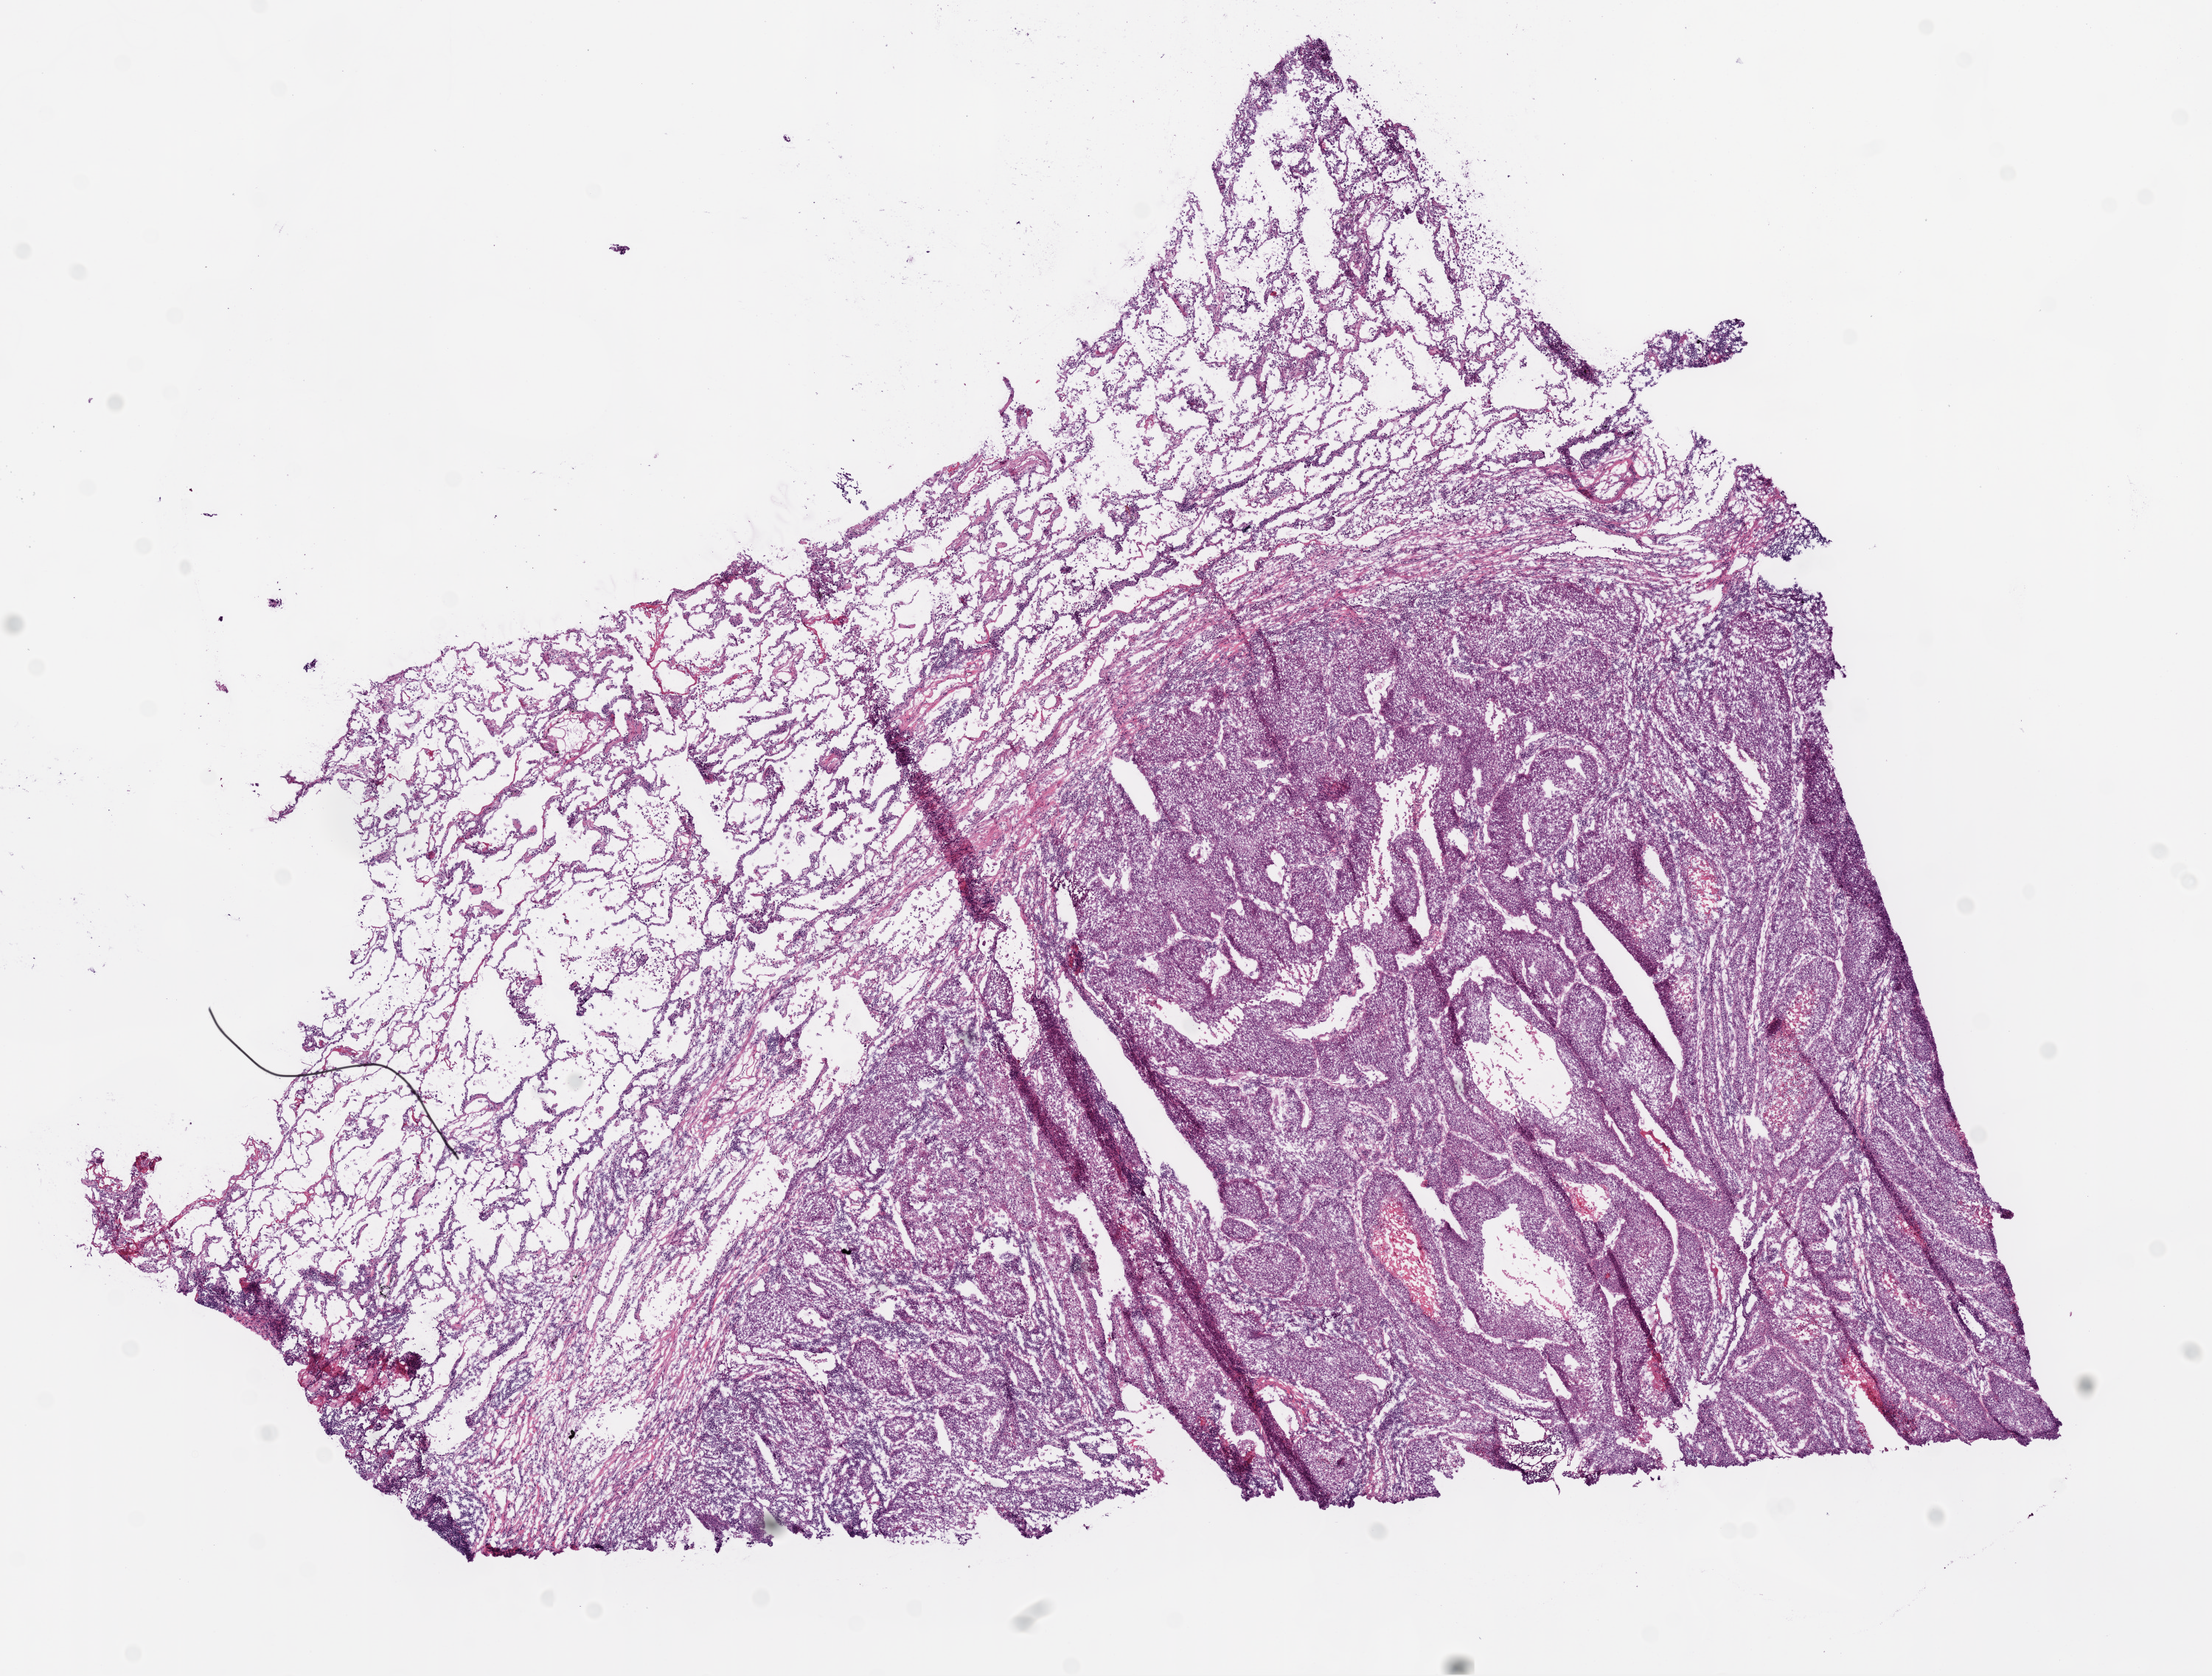
Digitized H&E tissue section (whole slide) — low-resolution overview of the scanned area, about 12.0 x 9.1 mm (acquisition: 20x scan); frozen section from the bottom of the tissue portion; primary tumour sample from the lung. Female, age 76 years at initial diagnosis. Pathologist review of this section (percent, as recorded): tumour cells 55%, tumour nuclei 70%, normal cells 35%, stromal cells 5%, necrosis 5%.
* TNM: T2 N0 M0
* laterality: left
* AJCC pathologic stage: IIA
* pathologic diagnosis: Squamous cell carcinoma, NOS (upper lobe, lung)